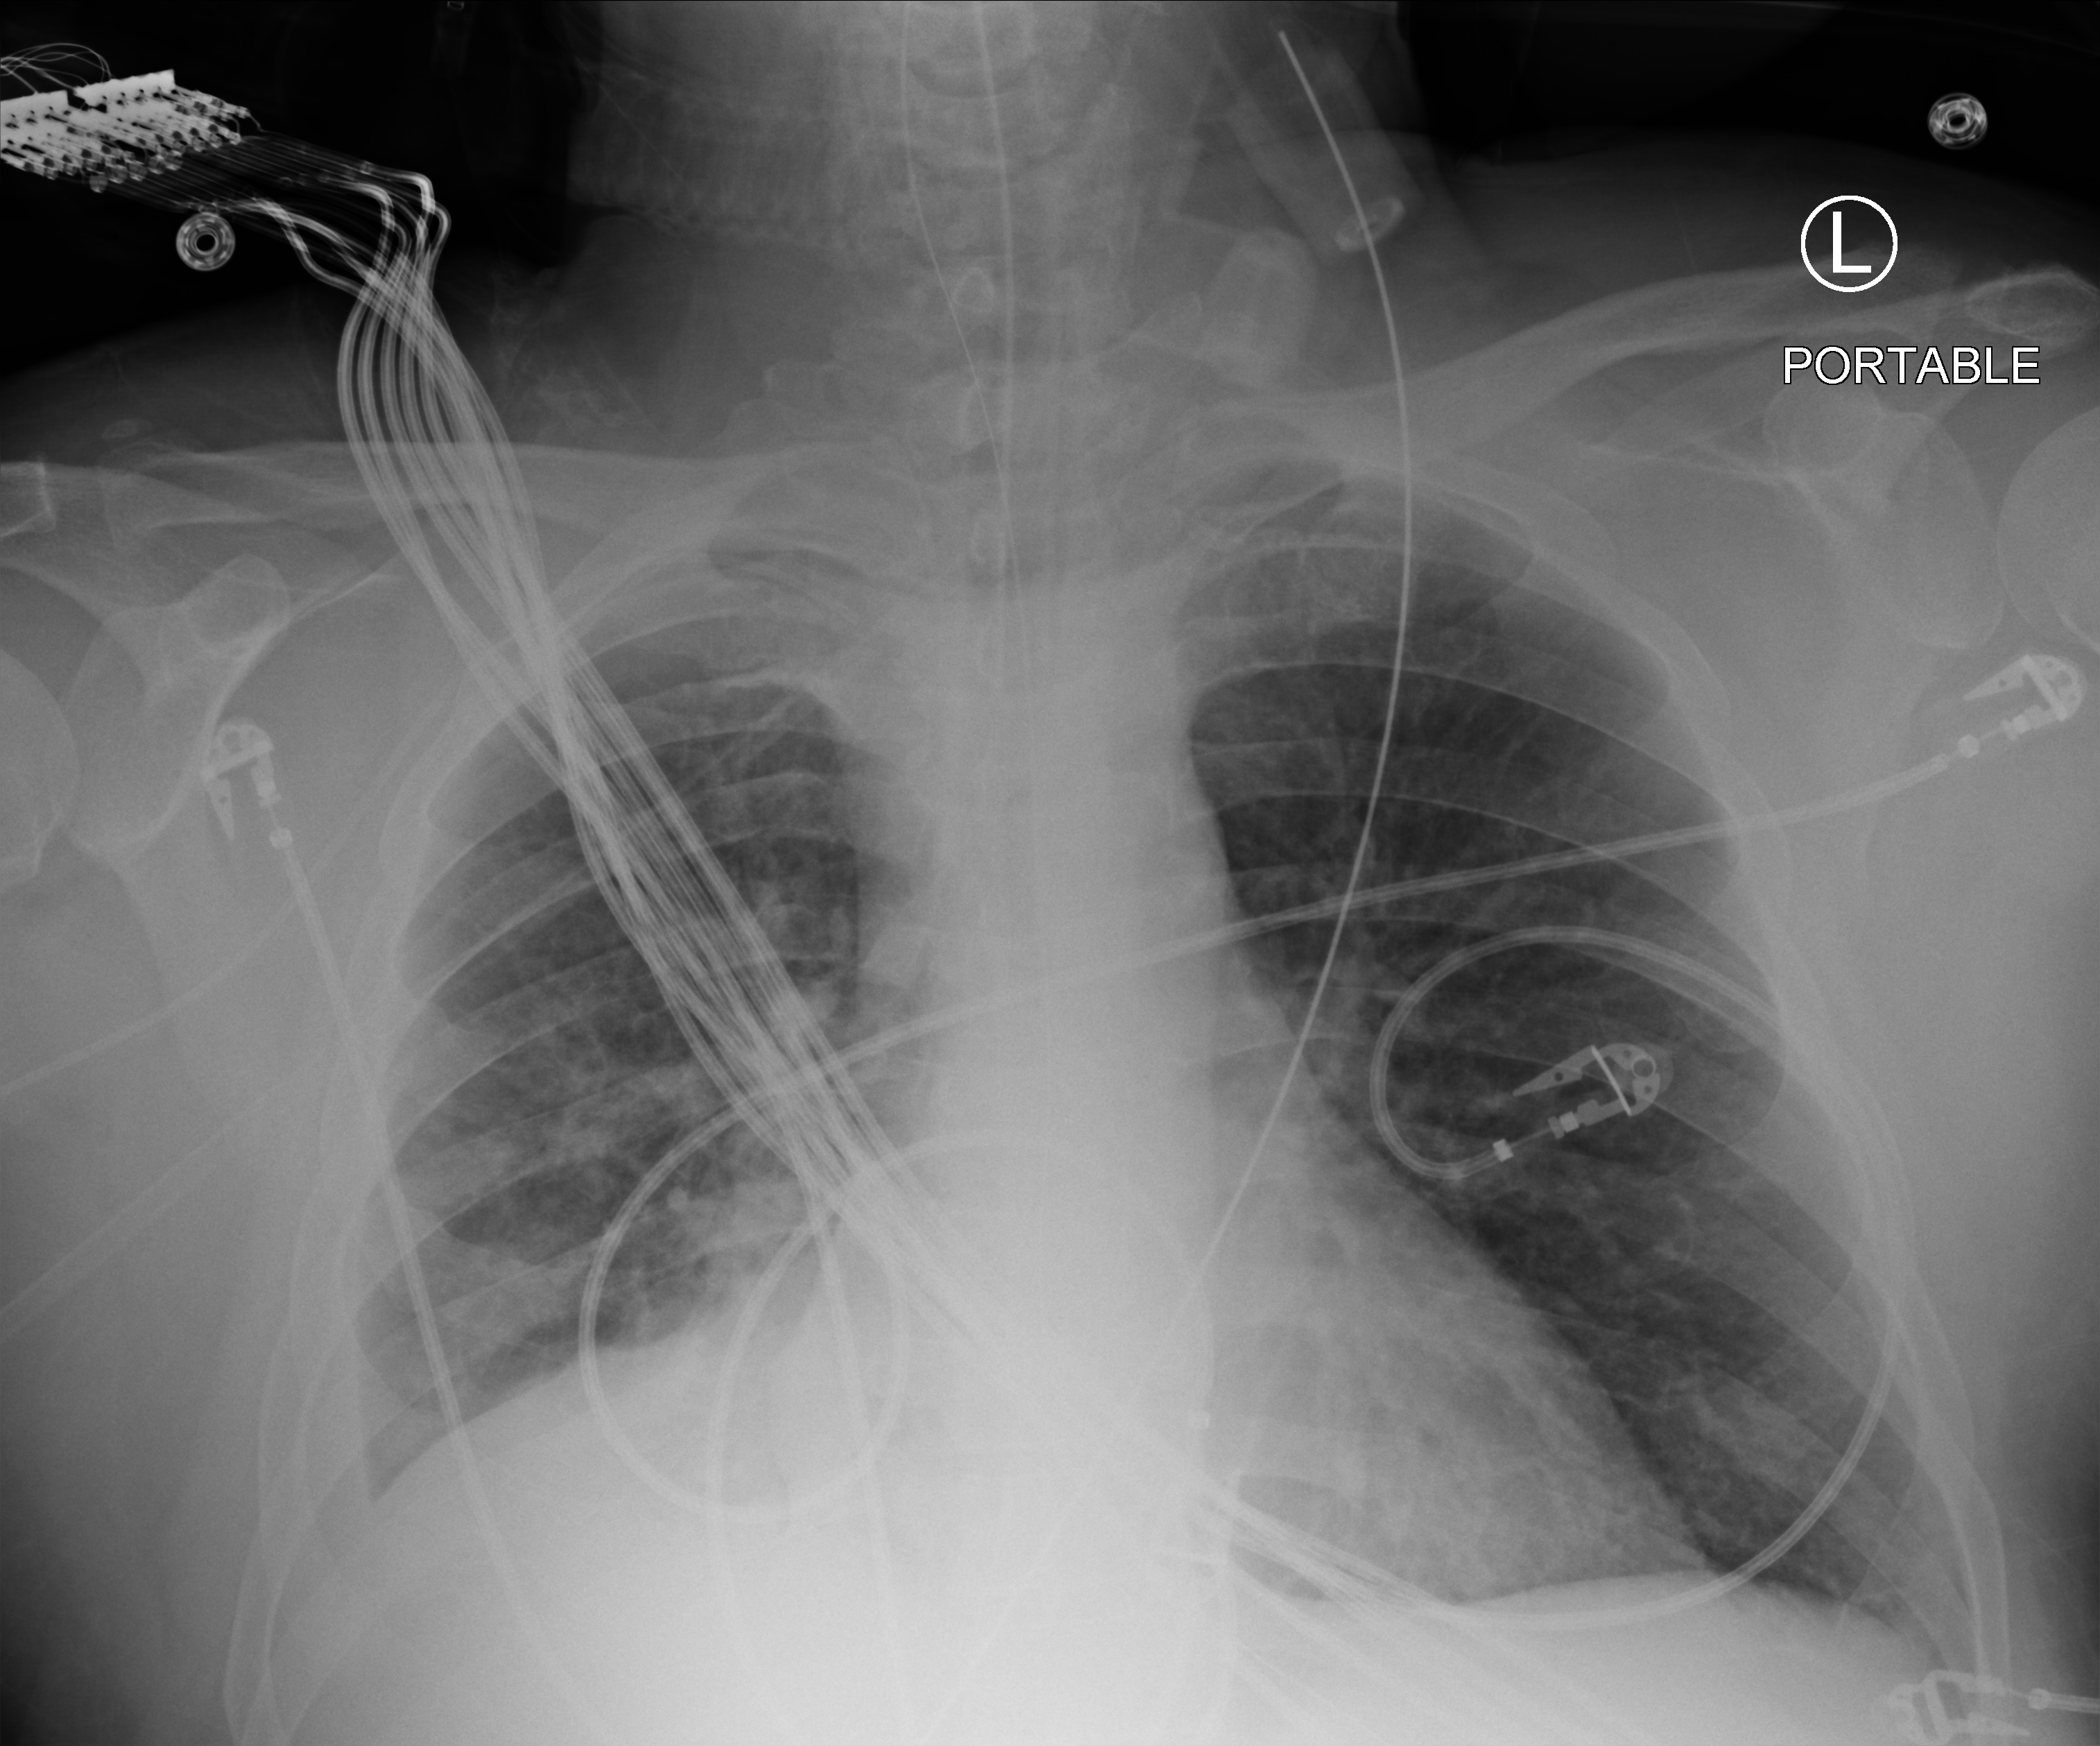
Portable chest radiograph, anteroposterior (AP) projection. Patient hospitalised with COVID-19; male, aged 18–59 years.
Hospital-stay facts (about this admission, not read from this image; timing relative to this image not recorded): admitted to intensive care during this hospital stay: yes; mechanically ventilated during this hospital stay: yes.